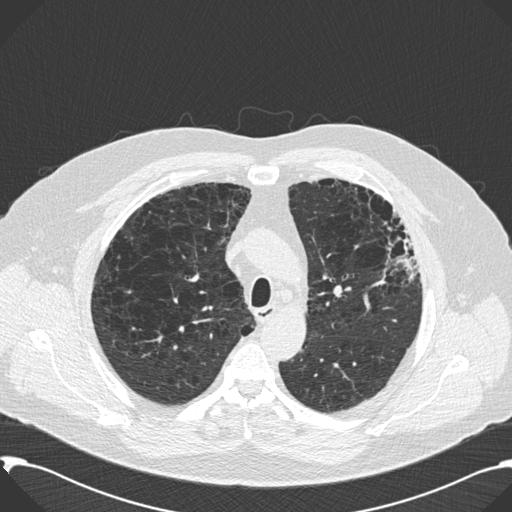
Low-dose screening chest CT, axial slice, second screening round (one year after baseline), lung window (W 1500 / L -600 HU), 120 kVp, slice 48 of 199 in the series, 512 × 512 image matrix, field of view 380 × 380 mm. Male, age 59 years at enrolment.
• Lesion marked by an expert reader, bounding box (x1, y1, x2, y2) in pixels: (362, 206, 422, 295).
• No non-calcified nodule or mass ≥4 mm was recorded by the screening reader at this exam.
• Official screen result: negative screen, significant abnormalities not suspicious for lung cancer.
• Lung cancer was diagnosed 518 days after this screen: bronchiolo-alveolar carcinoma, mixed mucinous and non-mucinous, left upper lobe, stage IA (AJCC 6th edition), 20 mm at pathology.